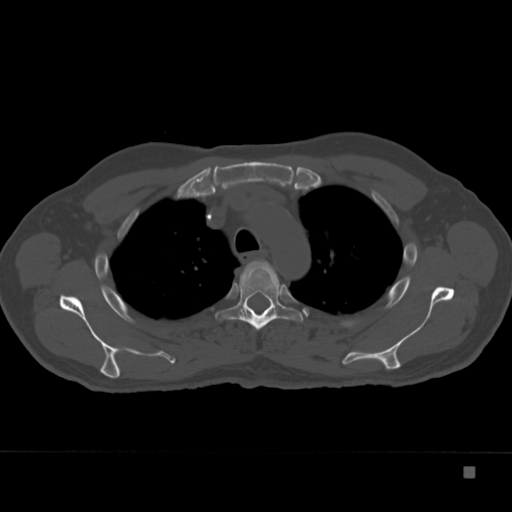
CT including the spine, one axial slice. Position 274 of 332 along the scan axis. Reconstruction kernel Br40s. 120 kVp. Bone window (W 1800 / L 400 HU). 1.5 mm slice thickness. 512 × 512 image matrix, field of view 389 × 389 mm. Male patient, age 72 years. Case-level facts recorded for this patient, not image findings: primary cancer: skeletal.
Structures marked on this image (semi-automatically segmented with operator editing):
- T3 vertebra: bounding box (x1, y1, x2, y2) in pixels: (239, 267, 278, 290)
- T4 vertebra: (214, 260, 303, 330)